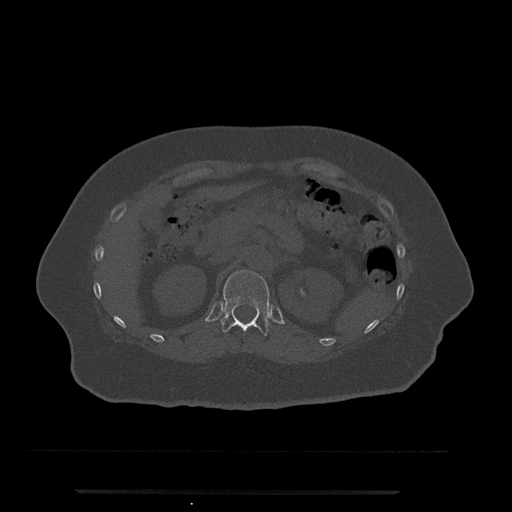
CT including the spine, one axial slice; position 171 of 797 along the scan axis; reconstruction kernel Br40s/3; bone window (W 1800 / L 400 HU); 0.5 mm slice thickness; 512 × 512 image matrix. Female patient, age 51 years. Case-level facts recorded for this patient, not image findings: primary cancer: neuro.
Outlined on this slice (semi-automatically segmented with operator editing):
- T12 vertebra: bounding box <221,270,270,336> (left, top, right, bottom; pixels)